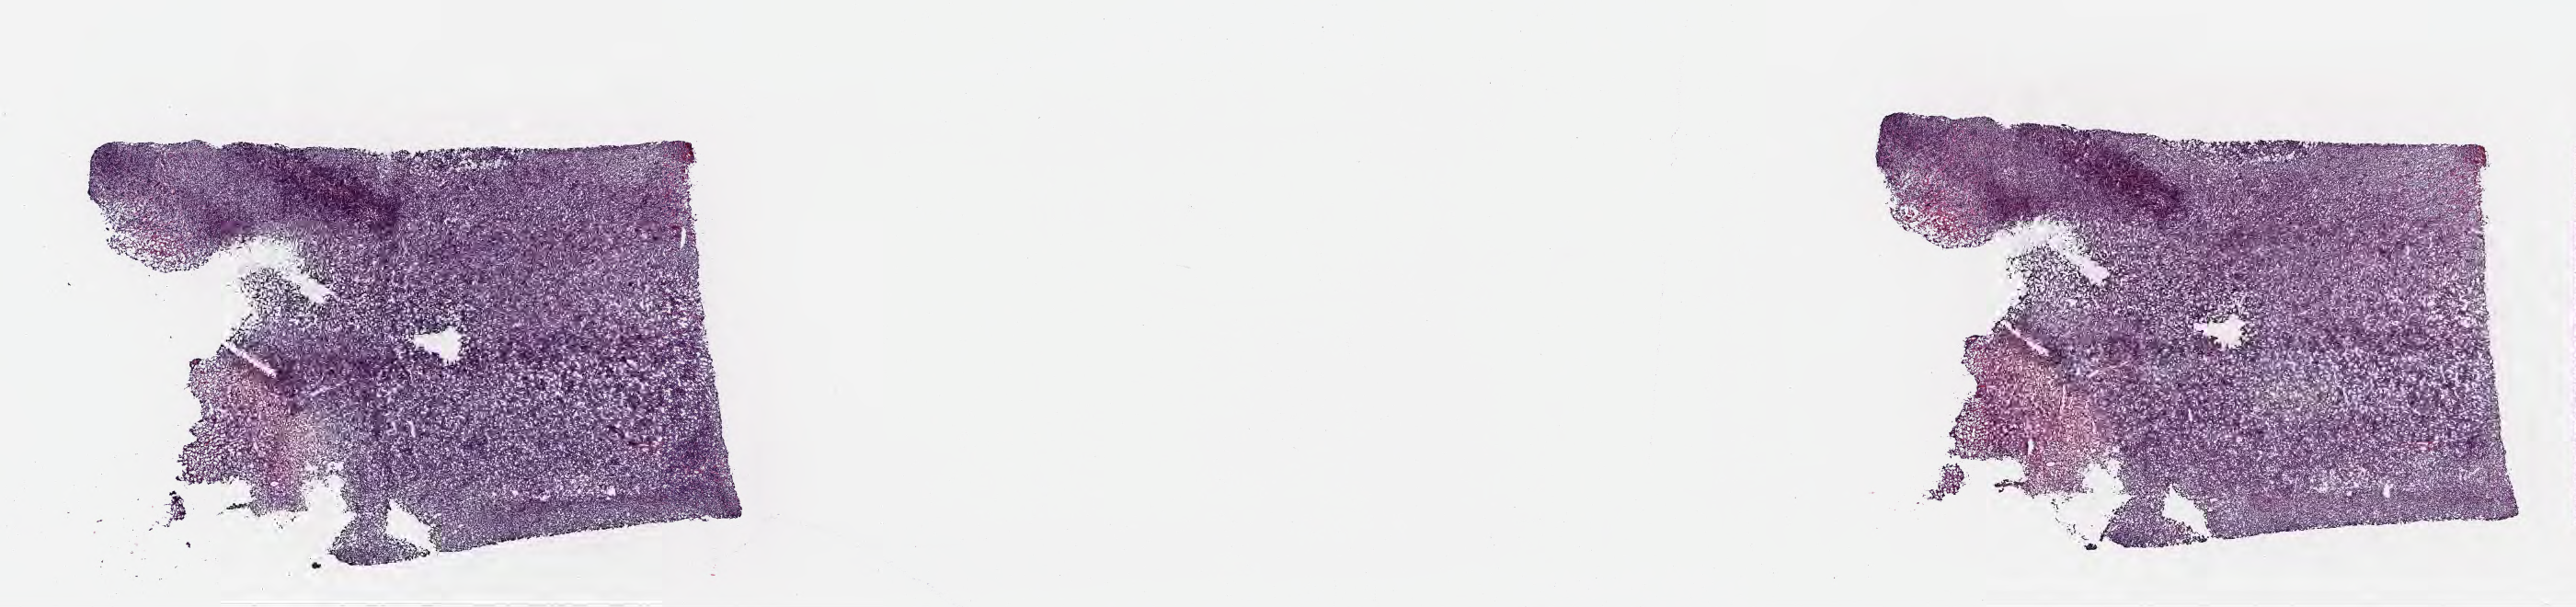
Hematoxylin and eosin (H&E) whole-slide image — shown as a low-resolution overview of the whole scanned area (about 22.6 x 5.3 mm). Cryosection. Specimen: primary tumor. Site: colon. Patient male; aged 14. Composition of this section per pathologist review: tumor cells 80%, tumor nuclei 85%, stromal cells 15%, necrosis 0%, normal cells 5%. Inflammatory infiltration, as recorded: lymphocyte infiltration 75%, monocyte infiltration 15%, neutrophil infiltration 5%.
Histologic diagnosis: Burkitt lymphoma, NOS. Ann Arbor stage (patient): Stage IV. Section: top of the tissue portion.